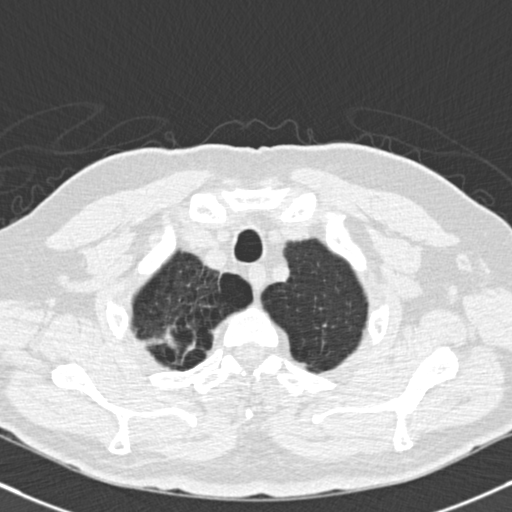
Low-dose screening chest CT, one axial slice. Position 146 of 165 along the scan axis. Reconstruction kernel B30f. 120 kVp. Lung window (W 1500 / L -600 HU). 2 mm slice thickness. 512 × 512 image matrix, field of view 324 × 324 mm.
Structures marked on this image (expert manual segmentation):
- lesion 1 (tumor, upper lobe of right lung): box from (x=157, y=327) to (x=180, y=354) px